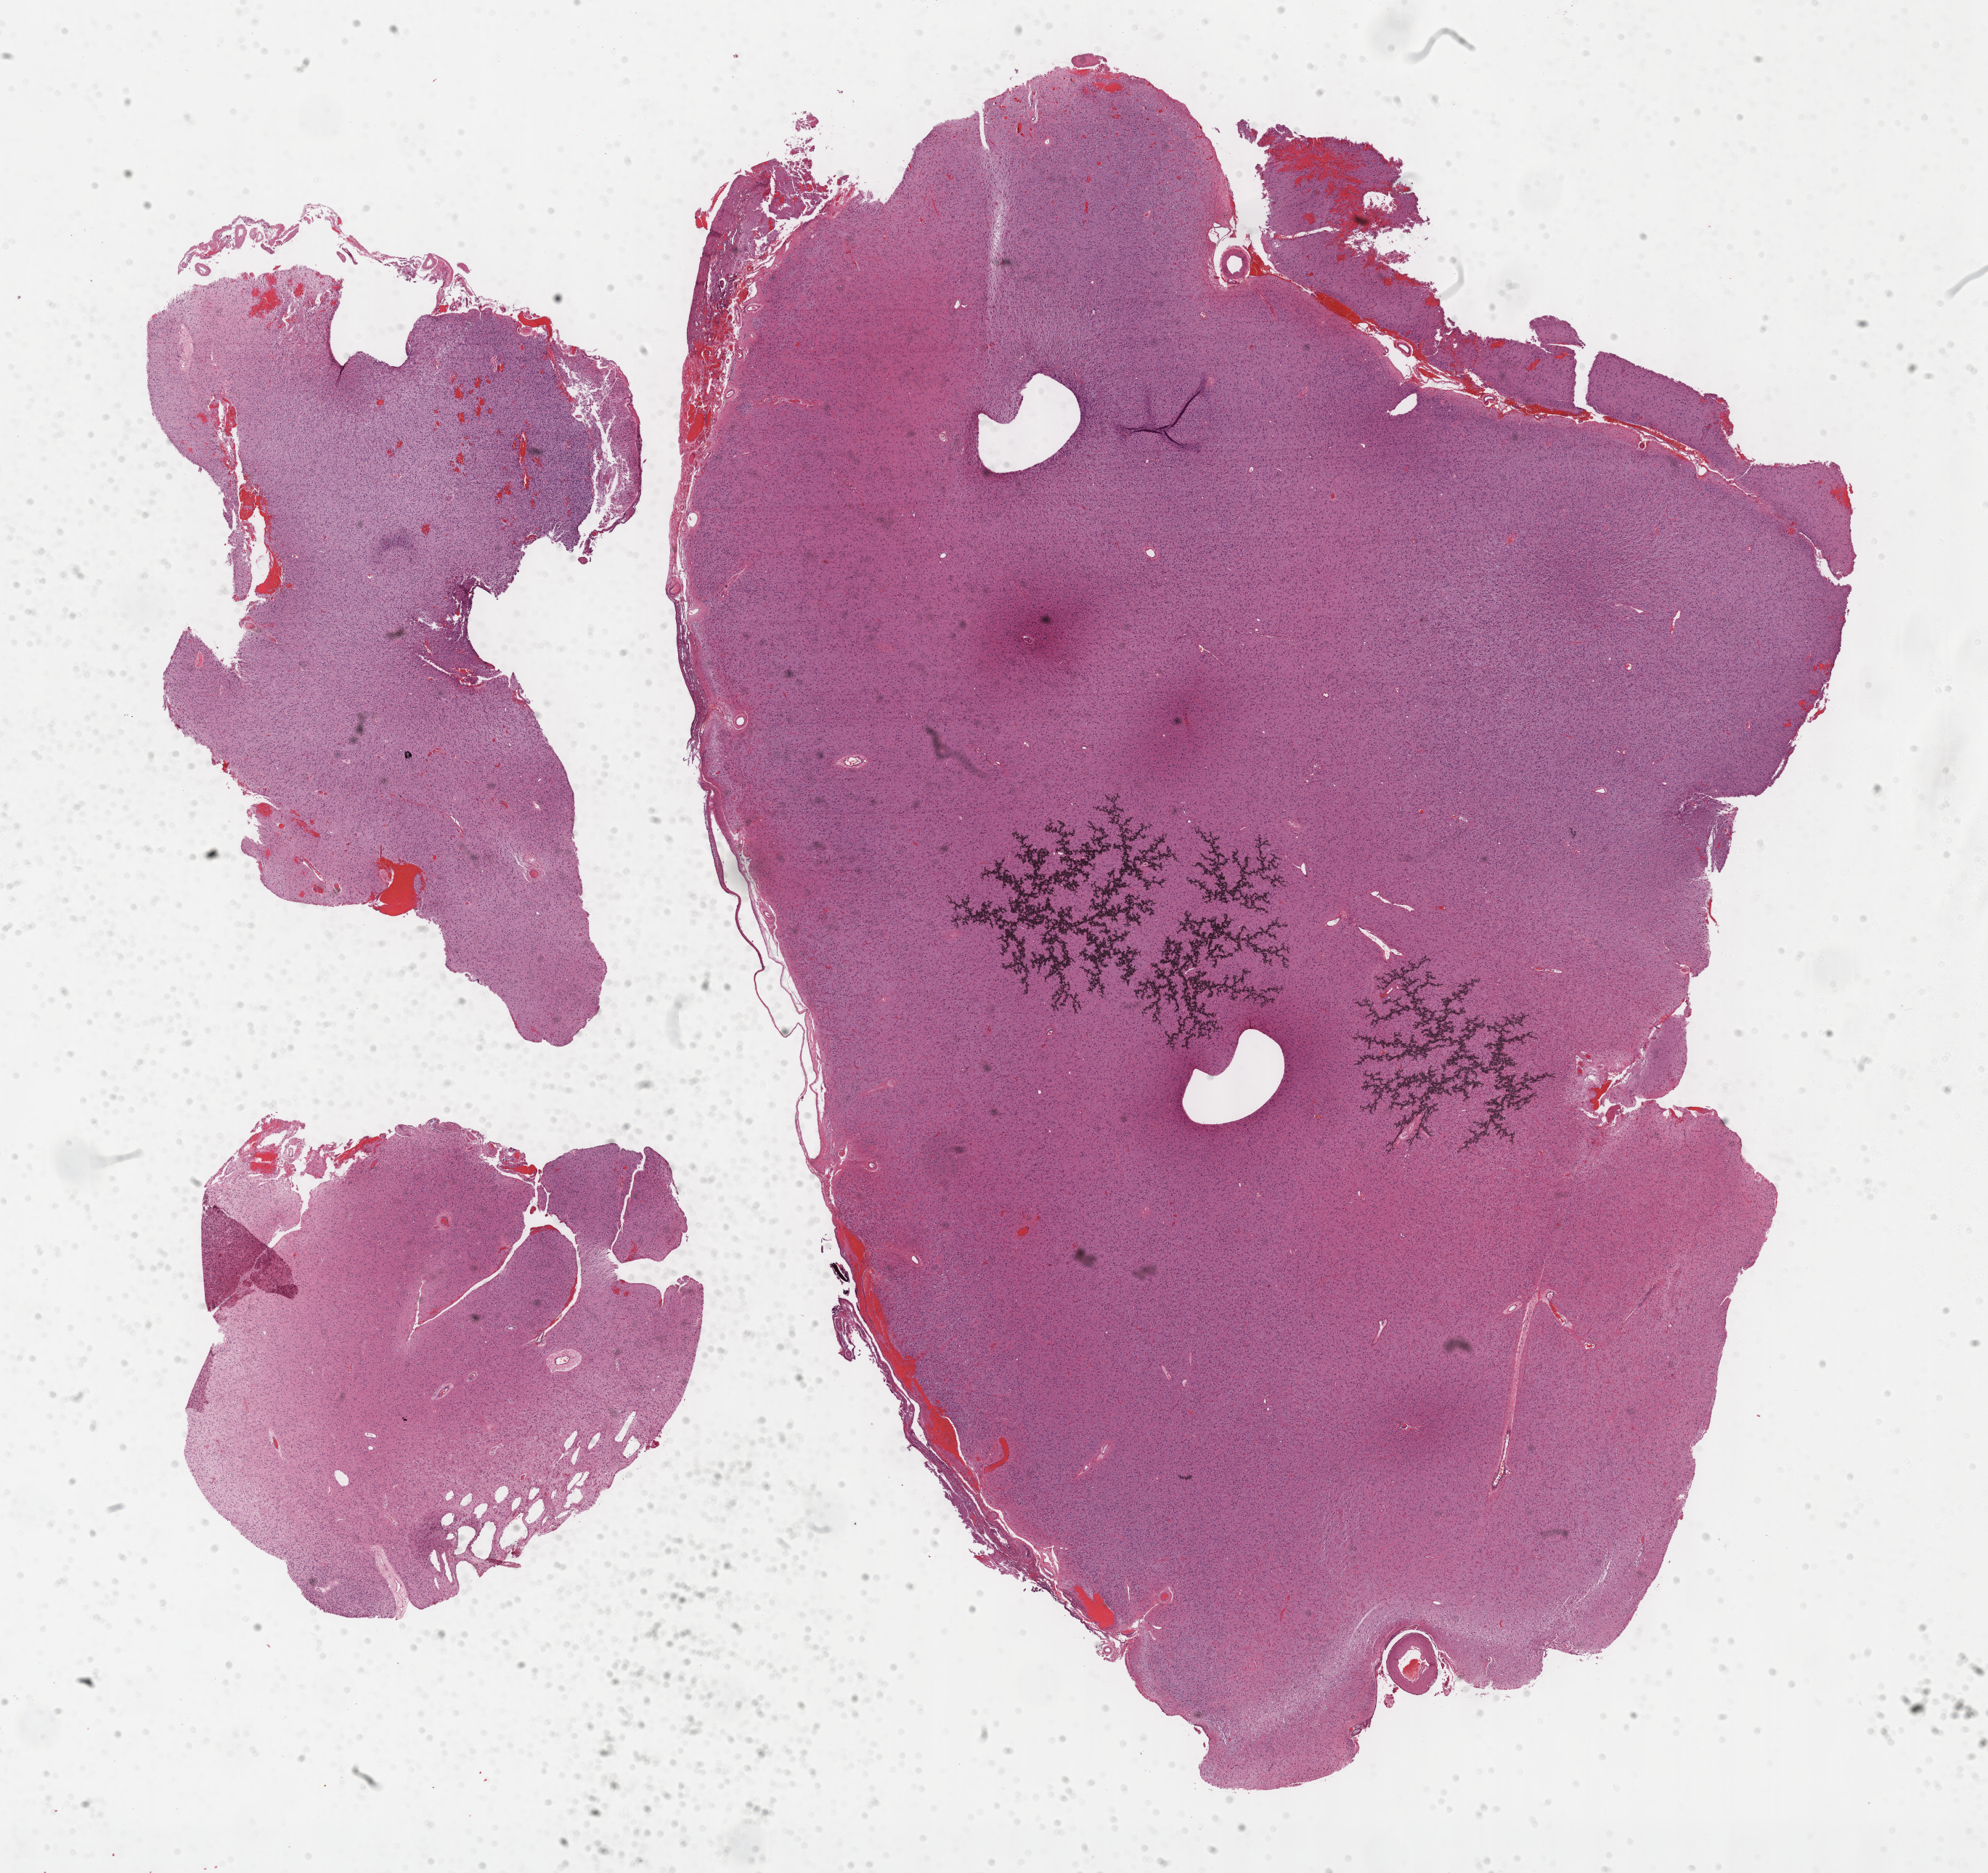
H&E whole-slide image — whole scanned area (about 22.1 x 20.9 mm) shown as a low-resolution overview. Formalin-fixed paraffin-embedded (FFPE) diagnostic section. Sample: primary tumour, brain. Female patient; age at initial diagnosis 58 years.
Diagnosis: Oligodendroglioma, NOS (cerebrum).